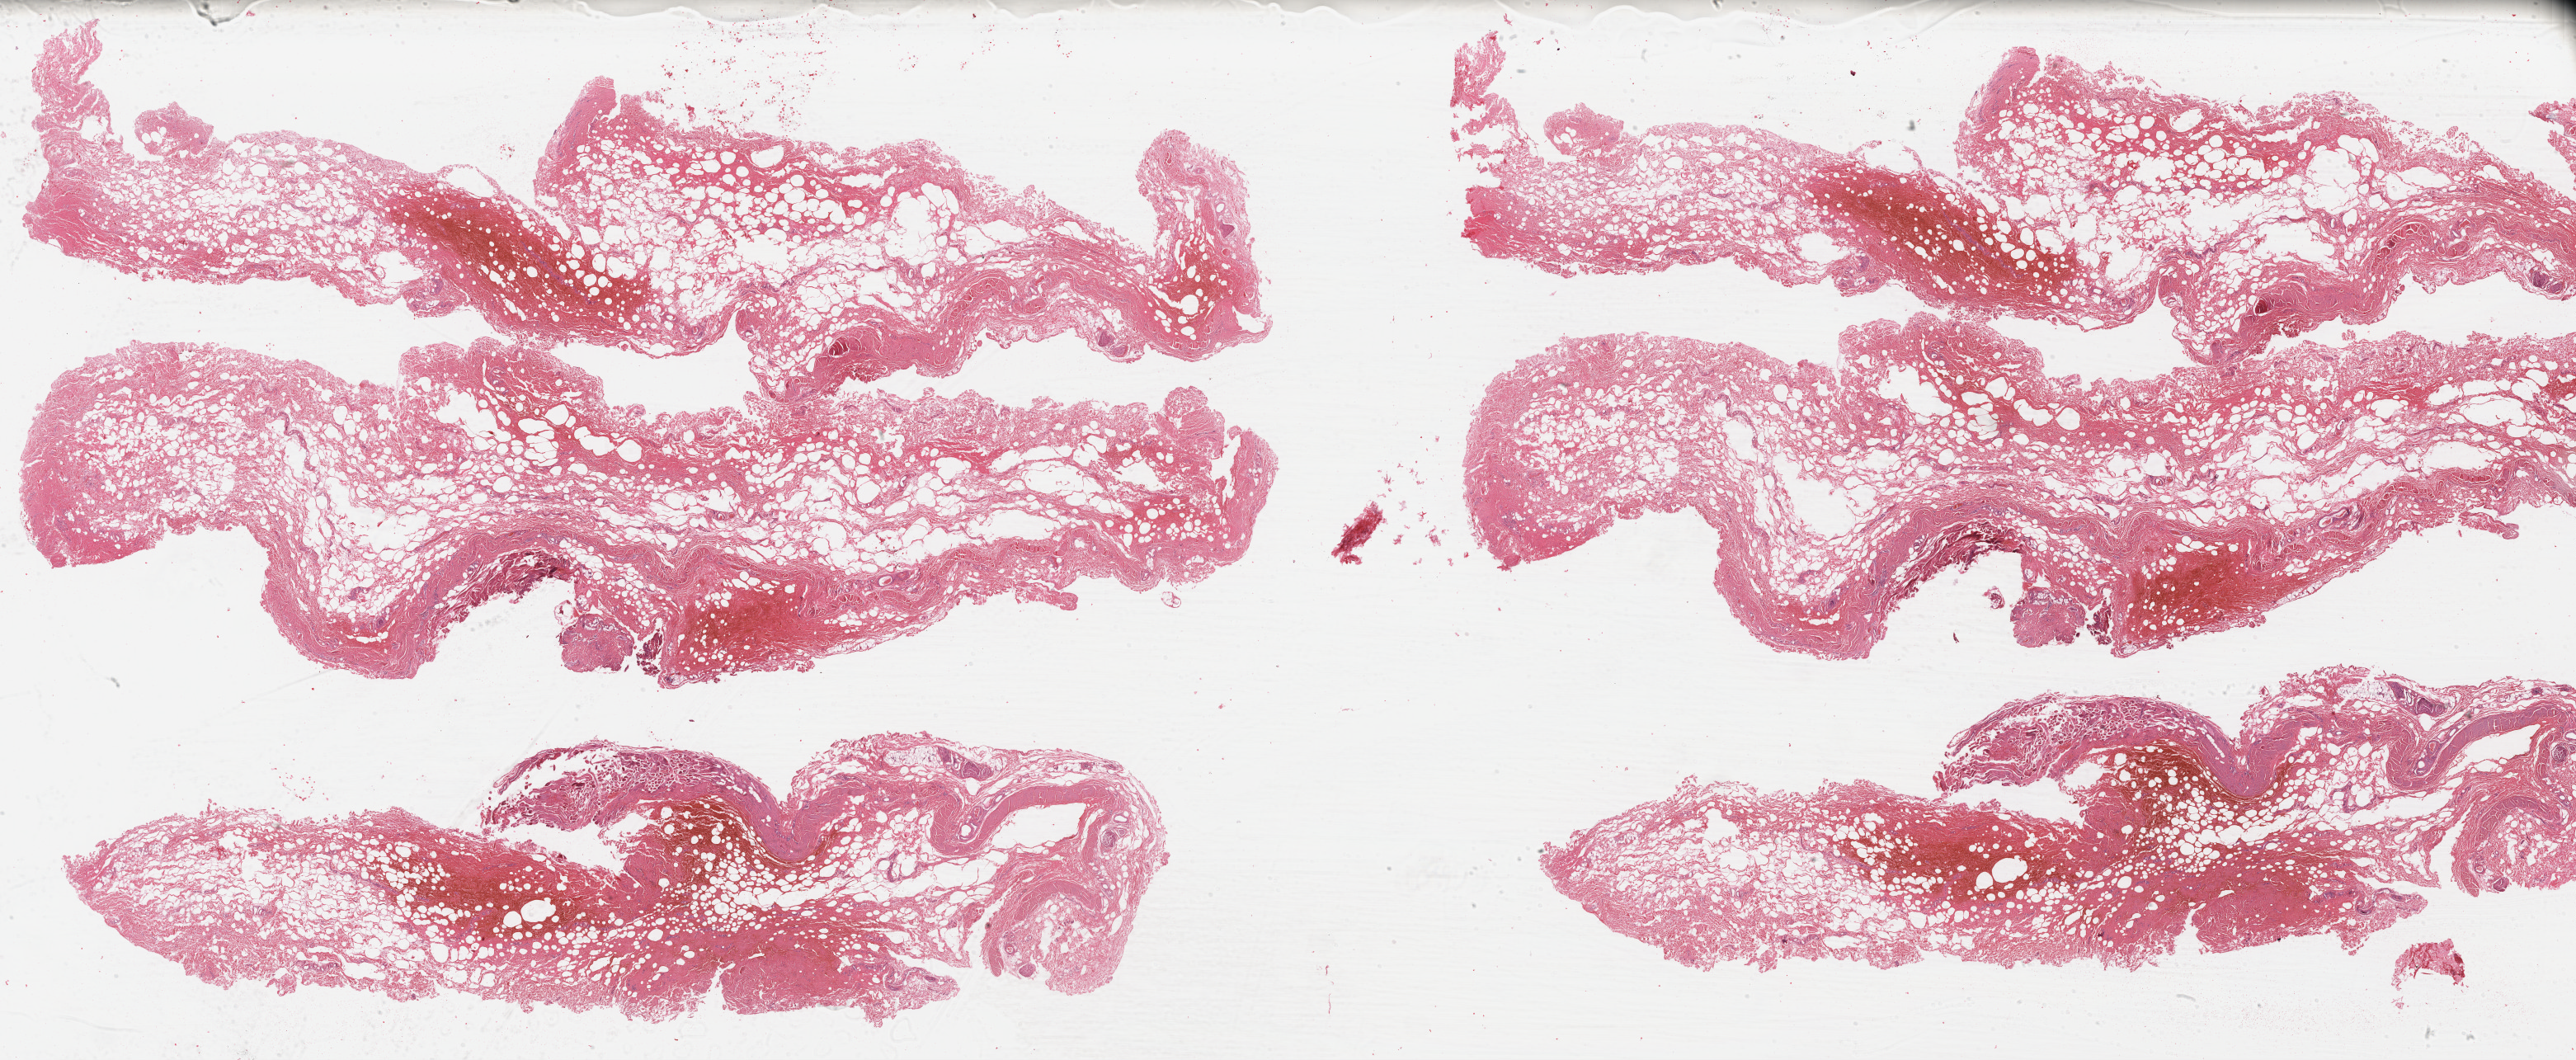
Digitized Hematoxylin and eosin (H&E) stained tissue section (whole slide), shown as a low-resolution overview of the whole scanned area (about 49.1 x 20.2 mm, acquisition: 40x scan); FFPE section; metastatic tumour sample. Male patient; age at initial diagnosis 19 years.
This section: metastatic tumour tissue. Patient diagnosis: Malignant melanoma, NOS.